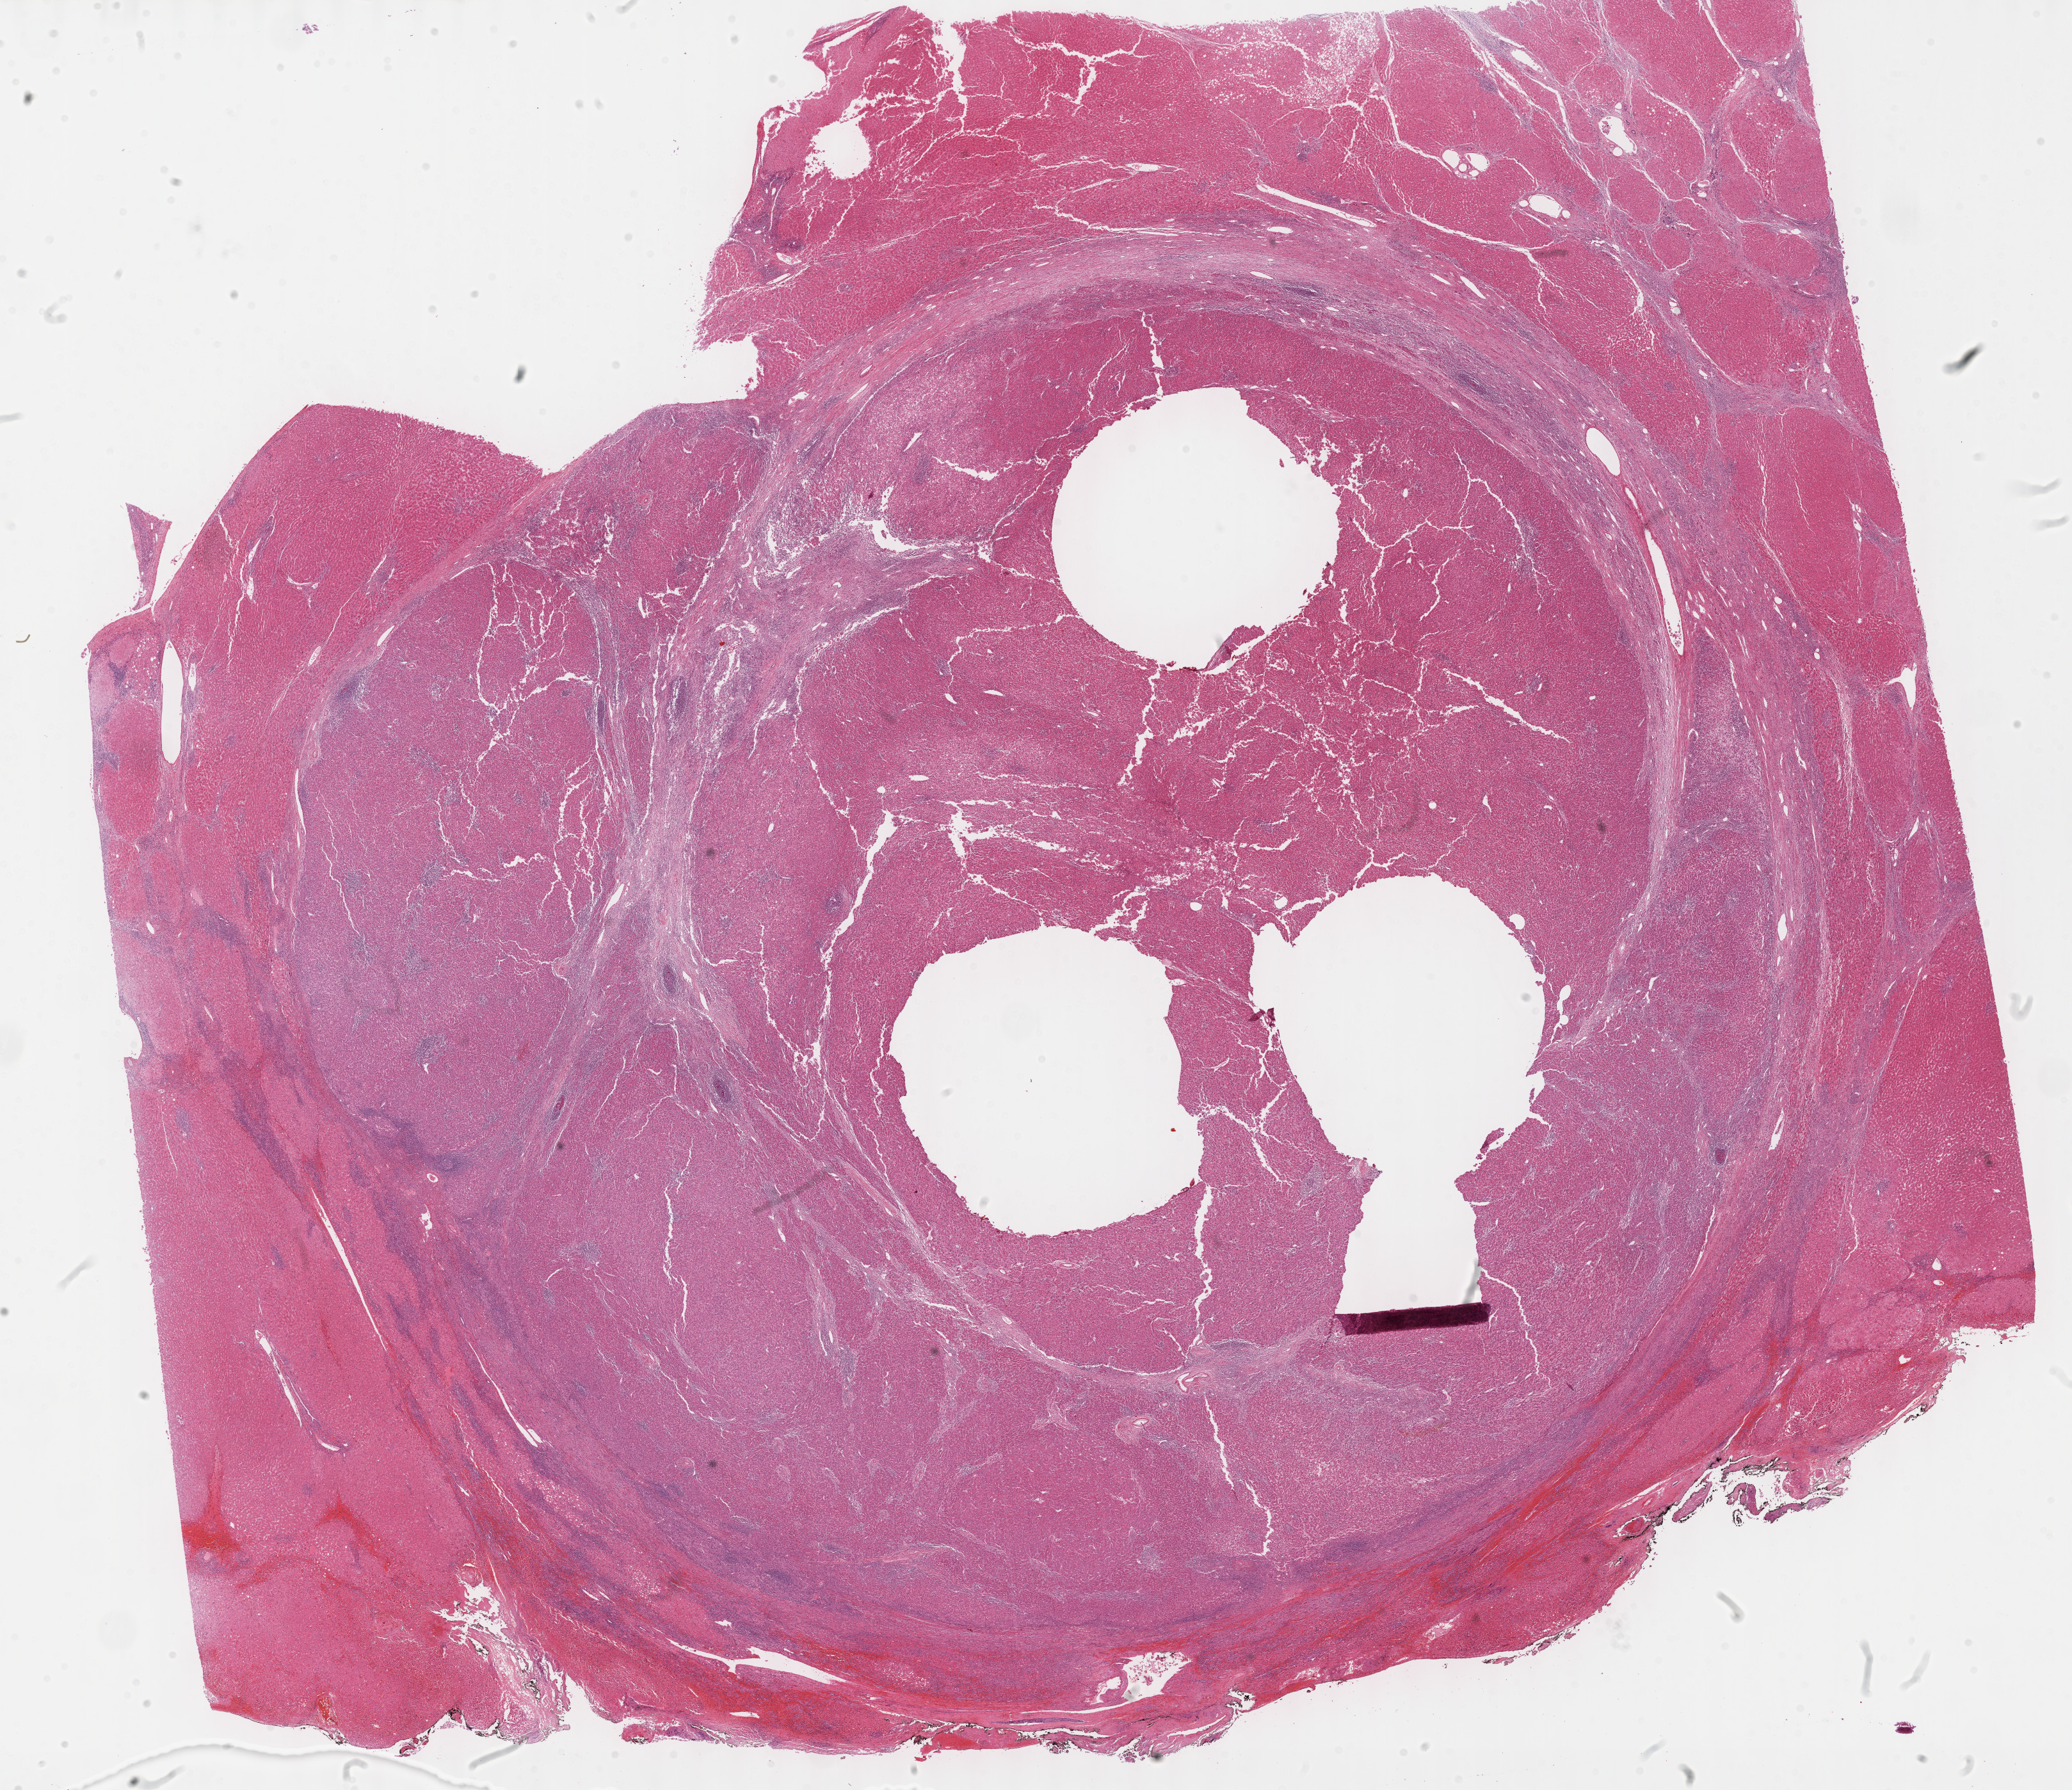
Digitized H&E tissue section (whole slide), shown as a low-resolution overview of the whole scanned area (about 26.2 x 22.6 mm); FFPE section; primary tumour sample from the liver. Male, age 61 years at initial diagnosis.
Pathologic diagnosis: Combined hepatocellular carcinoma and cholangiocarcinoma.